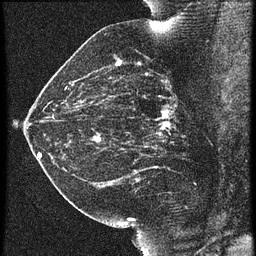
Breast MRI (dynamic contrast-enhanced), one sagittal slice; slice 31 of 60 in the series (ordered by position); 3 images stored at this slice position (order not interpretable as contrast timing); 1.5 T; TE 4.2 ms, TR 21.3 ms; 256 × 256 image matrix, field of view 180 × 180 mm. Female patient, age 42 years. From the clinical record (not read from this slice): setting: breast cancer imaged before/during neoadjuvant chemotherapy; receptor status: HER2-positive.
Outlined on this slice (semi-automatically segmented with operator editing):
- analysis volume of interest (the breast-tissue region the enhancement analysis was run in; not a lesion): bounding box (x1, y1, x2, y2) in pixels: (122, 82, 195, 147)
- tumour enhancement mask (voxels above the 90 % enhancement threshold inside the analysis volume of interest): (158, 106, 176, 129)